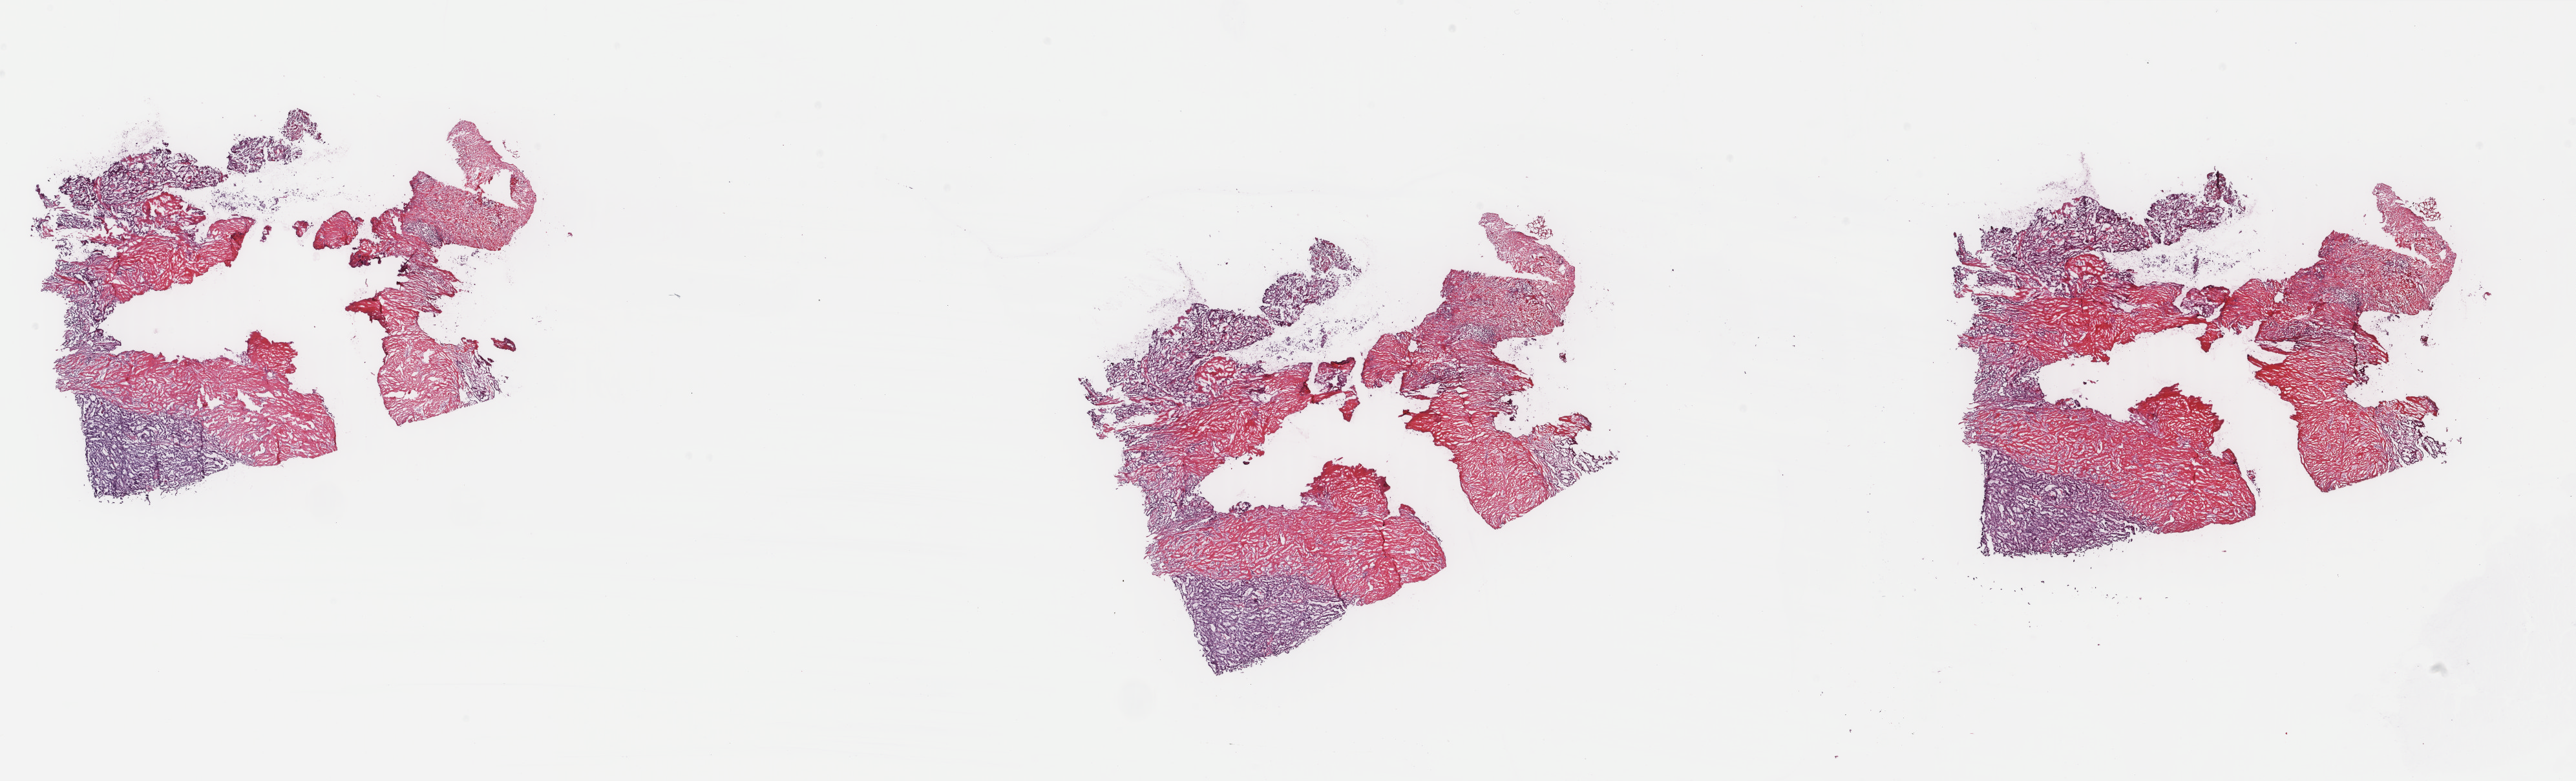
Whole-slide histology image, Hematoxylin and eosin (H&E) stained — shown as a low-resolution overview of the whole scanned area (about 31.6 x 9.6 mm, from a 40x scan), frozen section from the top of the tissue portion, thyroid, primary tumour sample. Patient sex: female. Pathologist review of this section (percent, as recorded): tumour cells 70%, tumour nuclei 70%, normal cells 0%, stromal cells 30%, necrosis 0%. Infiltration values recorded for this section: lymphocyte infiltration 5%, monocyte infiltration 0%, neutrophil infiltration 0%.
AJCC pathologic stage: IVA (7th edition). Lymph nodes positive (case pathology): 25 of 33 examined. Laterality: bilateral. Histologic diagnosis: Papillary carcinoma, columnar cell (thyroid gland).